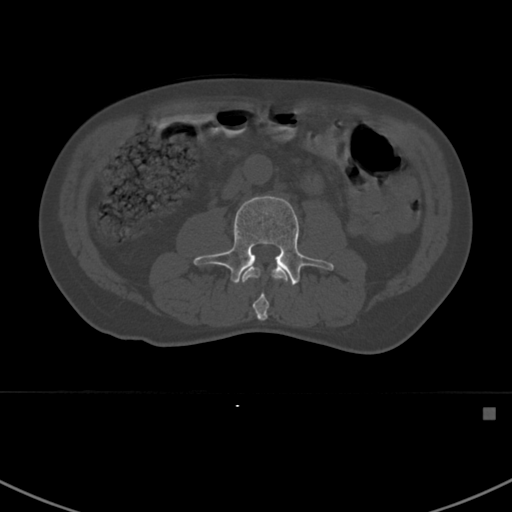
CT including the spine, one axial slice; position 269 of 412 along the scan axis; bone window (W 1800 / L 400 HU); 1.5 mm slice thickness; 512 × 512 image matrix. Male patient, age 59 years. Case-level facts recorded for this patient, not image findings: primary cancer: prostate.
Annotated regions visible in this slice (semi-automatically segmented with operator editing):
- L2 vertebra: bounding box (x1, y1, x2, y2) in pixels: (241, 266, 289, 321)
- L3 vertebra: (191, 195, 334, 285)